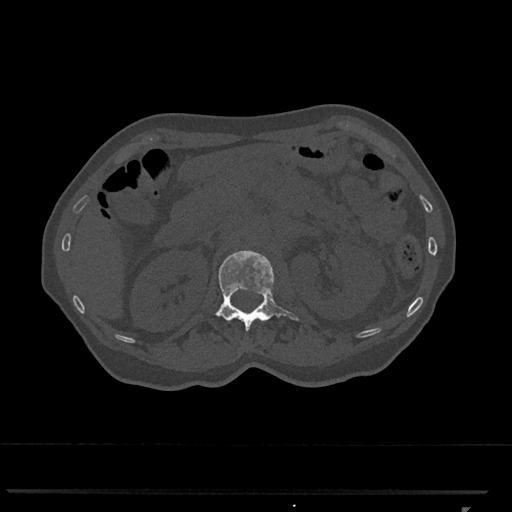
CT including the spine, one axial slice. Slice 403 of 793 in the series (ordered by position). Reconstruction kernel Br40s/3. 120 kVp. Bone window (W 1800 / L 400 HU). 0.5 mm slice thickness. 512 × 512 image matrix, field of view 380 × 380 mm. Female patient, age 62 years. From the clinical record (not read from this slice): primary cancer: renal.
Structures marked on this image (semi-automatically segmented with operator editing):
- L1 vertebra: box from (x=216, y=250) to (x=299, y=332) px